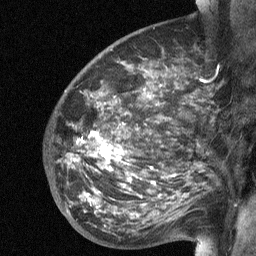
Breast MRI (dynamic contrast-enhanced), one sagittal slice. Position 40 of 64 along the scan axis. Dynamic contrast-enhanced study with each time point stored as its own series, time point 2 of 3 at this slice position (early post-contrast, ordered by acquisition time). 1.5 T. TE 4.8 ms, TR 27 ms. 256 × 256 image matrix, field of view 200 × 200 mm. Female patient, age 50 years. Case-level facts recorded for this patient, not image findings: setting: breast cancer imaged before/during neoadjuvant chemotherapy; receptor status: HER2-positive.
Annotated regions visible in this slice (semi-automatically segmented with operator editing):
- analysis volume of interest (the breast-tissue region the enhancement analysis was run in; not a lesion): box from (x=57, y=91) to (x=204, y=227) px
- tumour enhancement mask (voxels above the 90 % enhancement threshold inside the analysis volume of interest): (x=100, y=146)–(x=116, y=157)